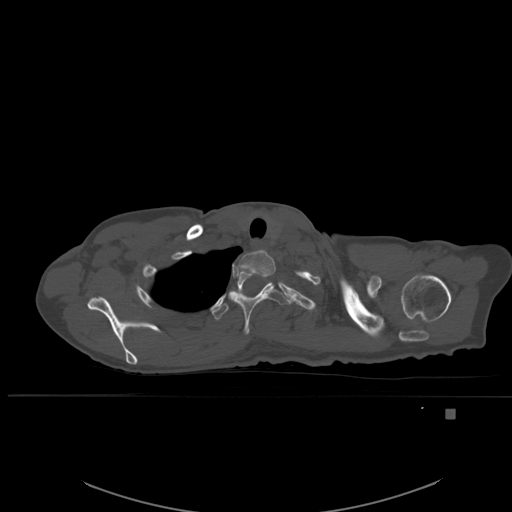
CT including the spine, one axial slice; position 437 of 537 along the scan axis; bone window (W 1800 / L 400 HU); 1.5 mm slice thickness; 512 × 512 image matrix, field of view 440 × 440 mm. Female patient, age 45 years. From the clinical record (not read from this slice): primary cancer: lung.
Annotated regions visible in this slice (semi-automatic segmentation, software-assisted and operator-edited):
- T1 vertebra: bounding box (x1, y1, x2, y2) in pixels: (234, 250, 276, 276)
- T2 vertebra: (228, 268, 290, 335)
- T3 vertebra: (212, 301, 229, 320)